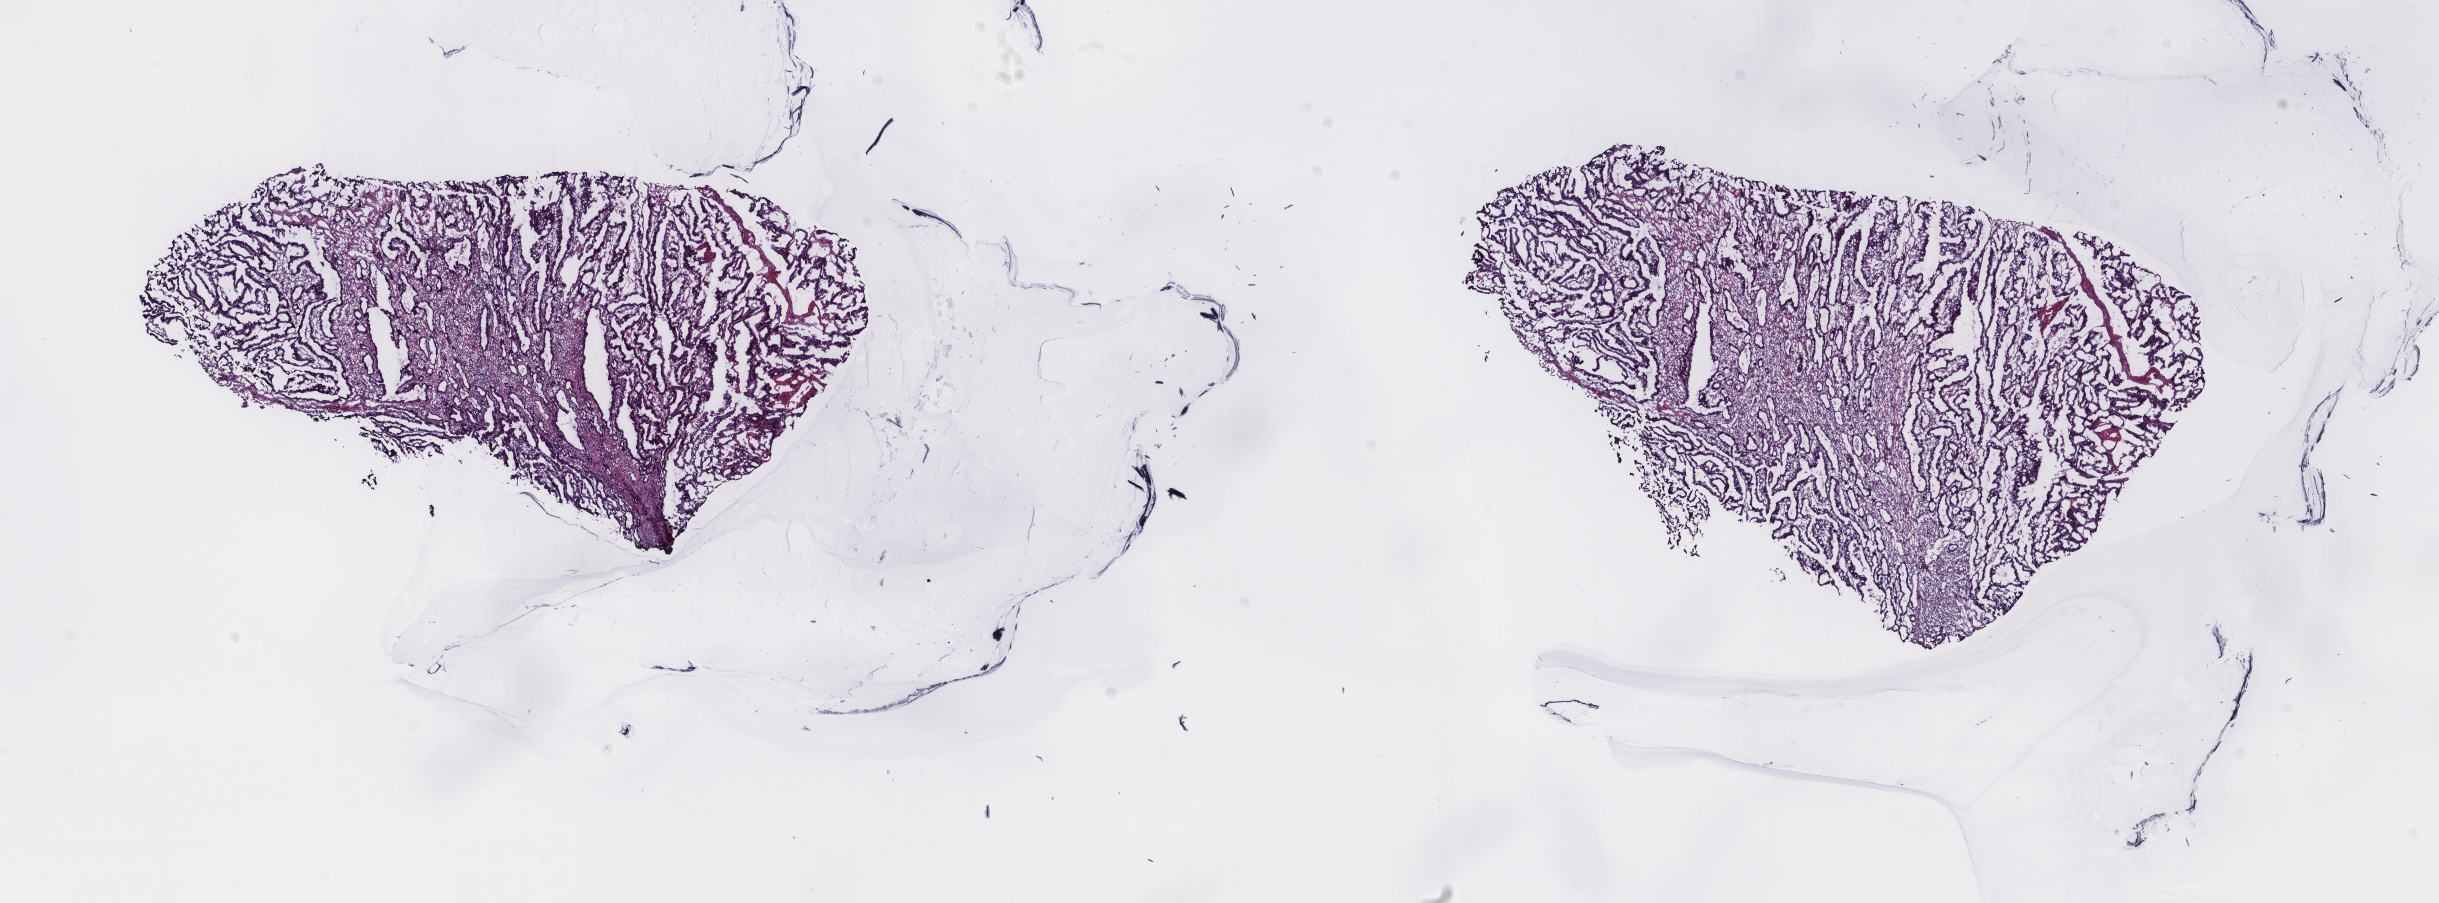
Digitized H&E-stained tissue section (whole slide), low-resolution overview of the scanned area, about 19.4 x 7.2 mm, frozen section from the top of the tissue portion, primary tumour sample from the colon. Patient: male, age at initial diagnosis 68 years.
Diagnosis: Adenocarcinoma, NOS.